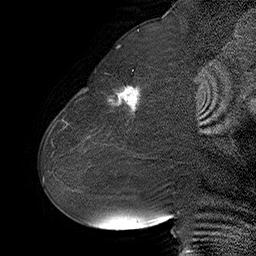
Breast MRI (dynamic contrast-enhanced), one sagittal slice. Slice 26 of 55 in the series (ordered by position). Dynamic contrast-enhanced series, time point 2 of 6 at this slice position (early post-contrast). 1.5 T. TE 4.5 ms, TR 32.4 ms. 3 mm slice thickness. 256 × 256 image matrix, field of view 180 × 180 mm. Female patient. Case-level facts recorded for this patient, not image findings: setting: breast cancer imaged before/during neoadjuvant chemotherapy; receptor status: HER2-positive.
Structures marked on this image (semi-automatic segmentation, software-assisted and operator-edited):
- analysis volume of interest (the breast-tissue region the enhancement analysis was run in; not a lesion): bounding box [x1, y1, x2, y2] px = [80, 64, 163, 134]
- tumour enhancement mask (voxels above the 100 % enhancement threshold inside the analysis volume of interest): [84, 86, 139, 113]